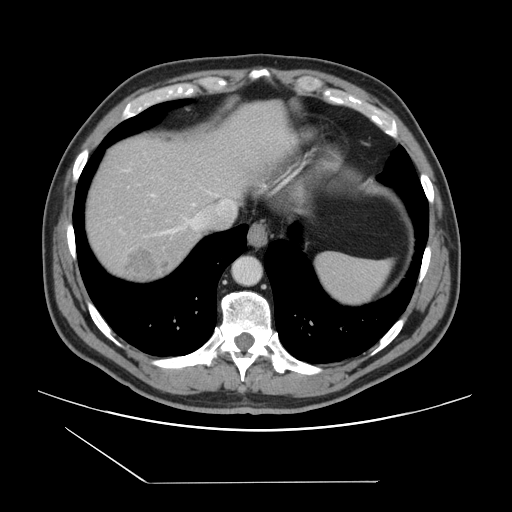
Contrast-enhanced abdominal CT, one axial slice. Position 127 of 157 along the scan axis. 120 kVp. Intravenous contrast given. Soft-tissue window (W 400 / L 40 HU). 2.5 mm slice thickness. 512 × 512 image matrix. Male patient, age 61 years. Case-level facts recorded for this patient, not image findings: diagnosis: colorectal cancer liver metastases, imaged before liver resection; multiple liver metastases: yes; largest metastasis: 5.5 cm; disease in both lobes: yes.
Outlined on this slice (outlined manually by an expert reader):
- hepatic veins: bounding box <152,200,236,236> (left, top, right, bottom; pixels)
- liver: <85,103,295,284>
- planned liver remnant (the part of the liver to remain after resection): <85,121,231,231>
- liver metastasis: <120,245,172,282>